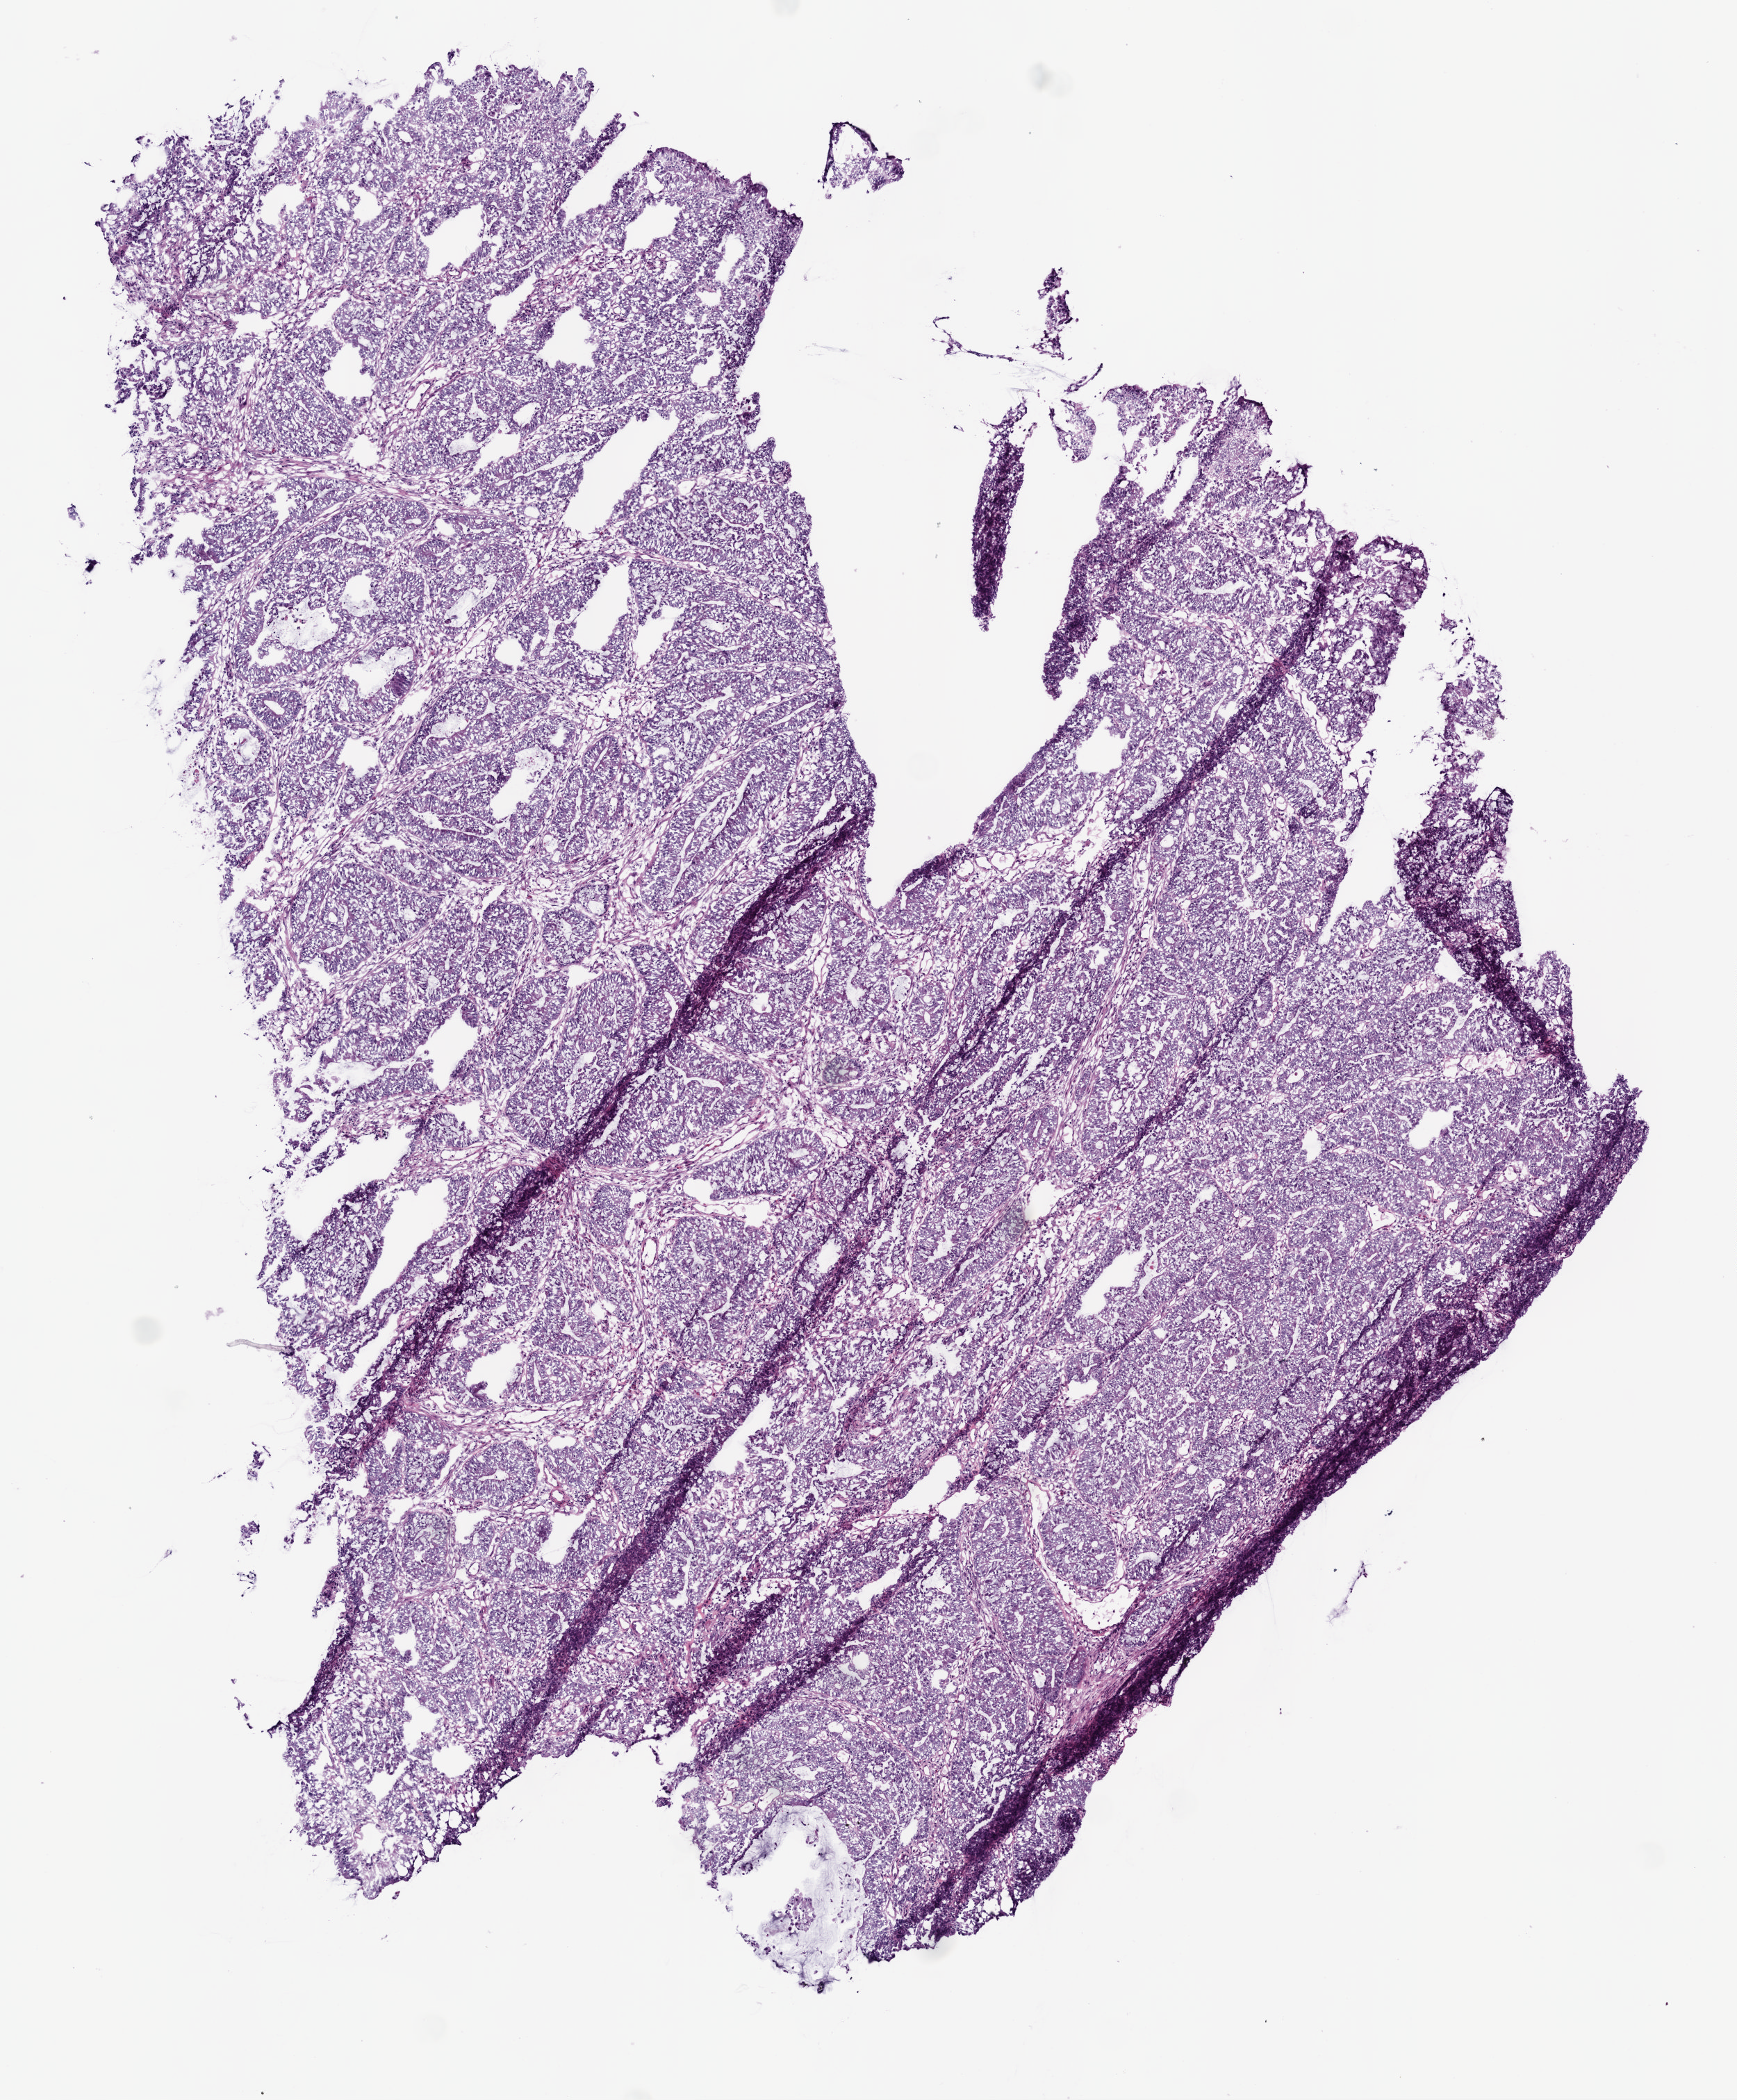
Whole-slide histology image, H&E-stained, whole scanned area (about 5.0 x 6.1 mm) shown as a low-resolution overview. Frozen section from the bottom of the tissue portion. Primary tumour sample from the colon. Male patient; age at initial diagnosis 68 years. Slide review estimates, as recorded: tumour cells 90%, tumour nuclei 95%, normal cells 0%, stromal cells 10%, necrosis 0%.
- diagnosis: Adenocarcinoma, NOS (sigmoid colon)
- TNM: T3 N0 M0
- AJCC pathologic stage: II